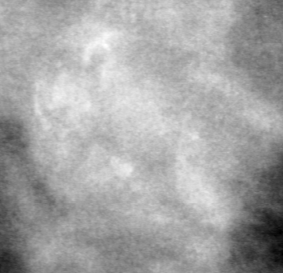
Region of interest cut from a scanned film mammogram (one marked finding); left breast; CC view; BI-RADS breast density category 4 (scale 1–4).
Marked abnormality: calcifications, morphology pleomorphic, distribution clustered; BI-RADS assessment category 4; subtlety rating 3 on a 1 (subtle) to 5 (obvious) scale; pathology (as recorded): malignant.